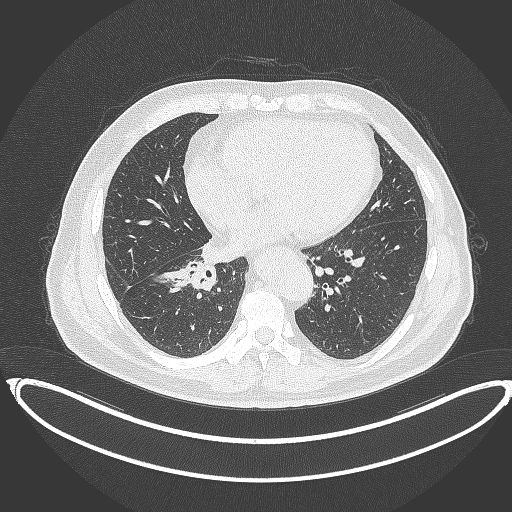
Chest CT, one axial slice; position 163 of 387 along the scan axis; lung window (W 1500 / L -600 HU); 512 × 512 image matrix, field of view 448 × 448 mm. Patient: male, 61 years. Case-level facts recorded for this patient, not image findings: clinical TNM (as recorded): T1b N1 M0.
Outlined on this slice (rectangle marked by the reading radiologist):
- lung tumour (recorded histology: squamous cell carcinoma): bounding box [x1, y1, x2, y2] px = [153, 259, 216, 297]